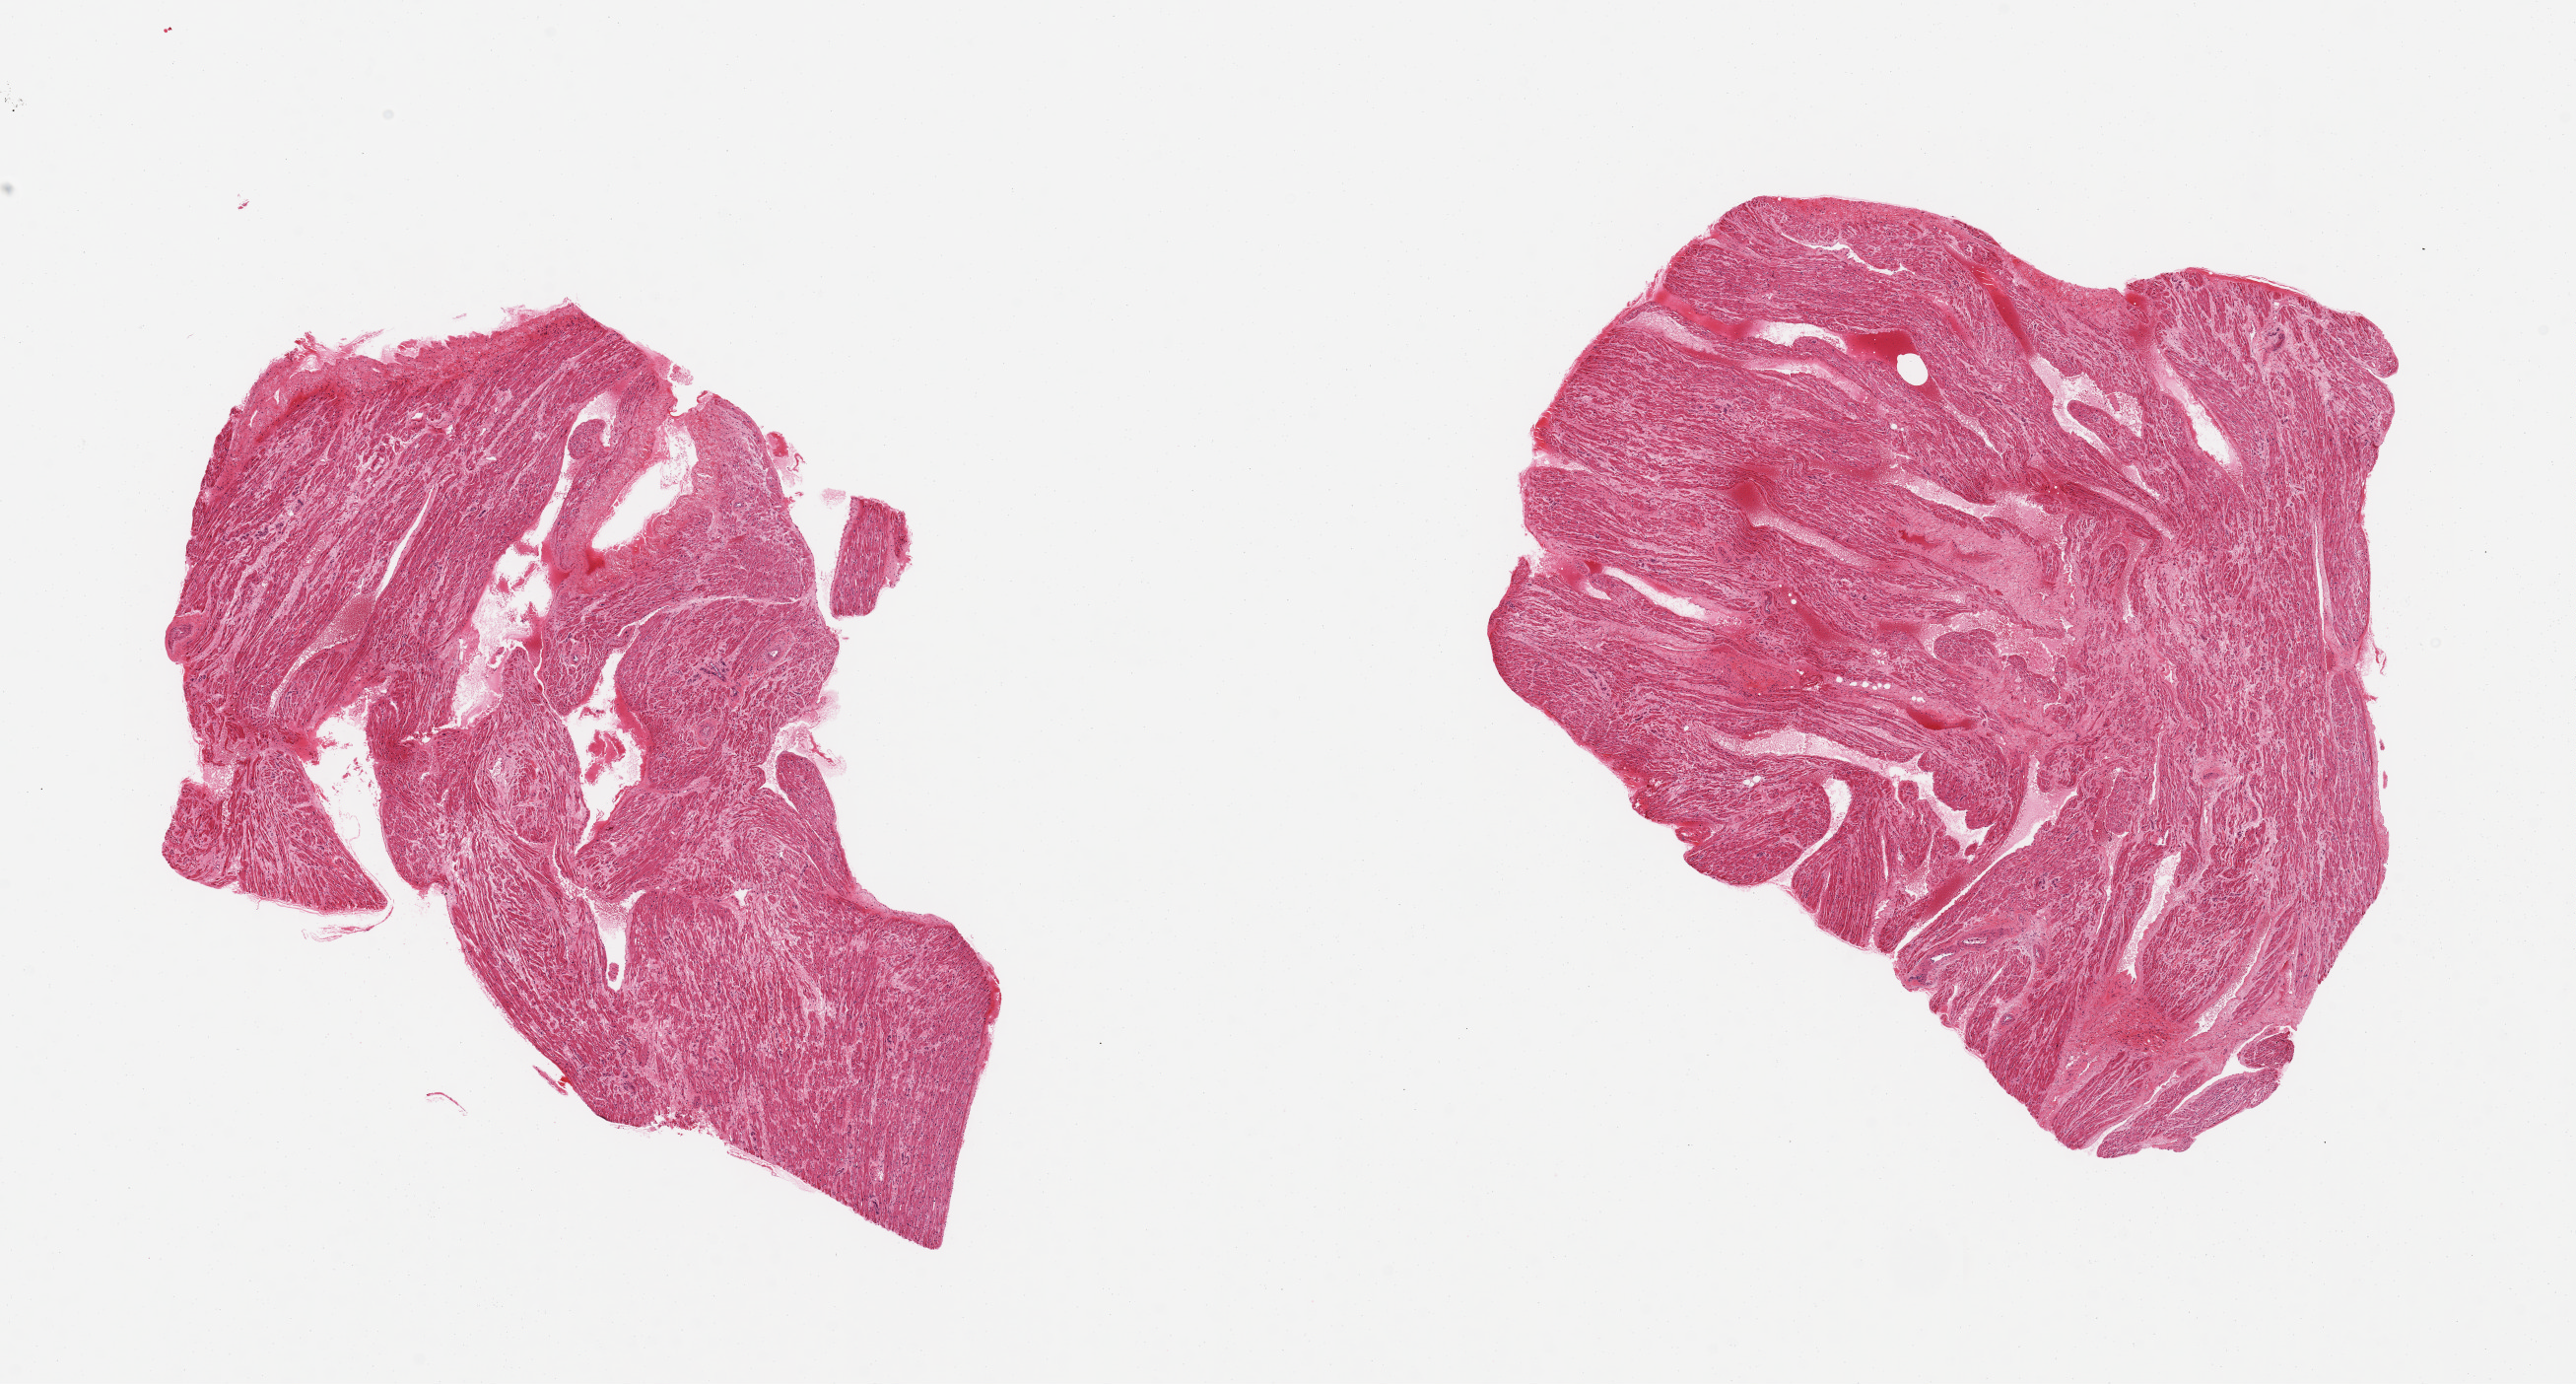
Digitized H&E-stained section, brightfield, low-resolution overview of the scanned area, about 20.7 x 11.1 mm (acquisition: 20x scan); PAXgene-fixed, paraffin-embedded tissue; section of auricular appendage (target tissue); tissue donor sample. Donor: female.
Pathologist's review note for this sample: 2 pieces, no significant abnormalities.